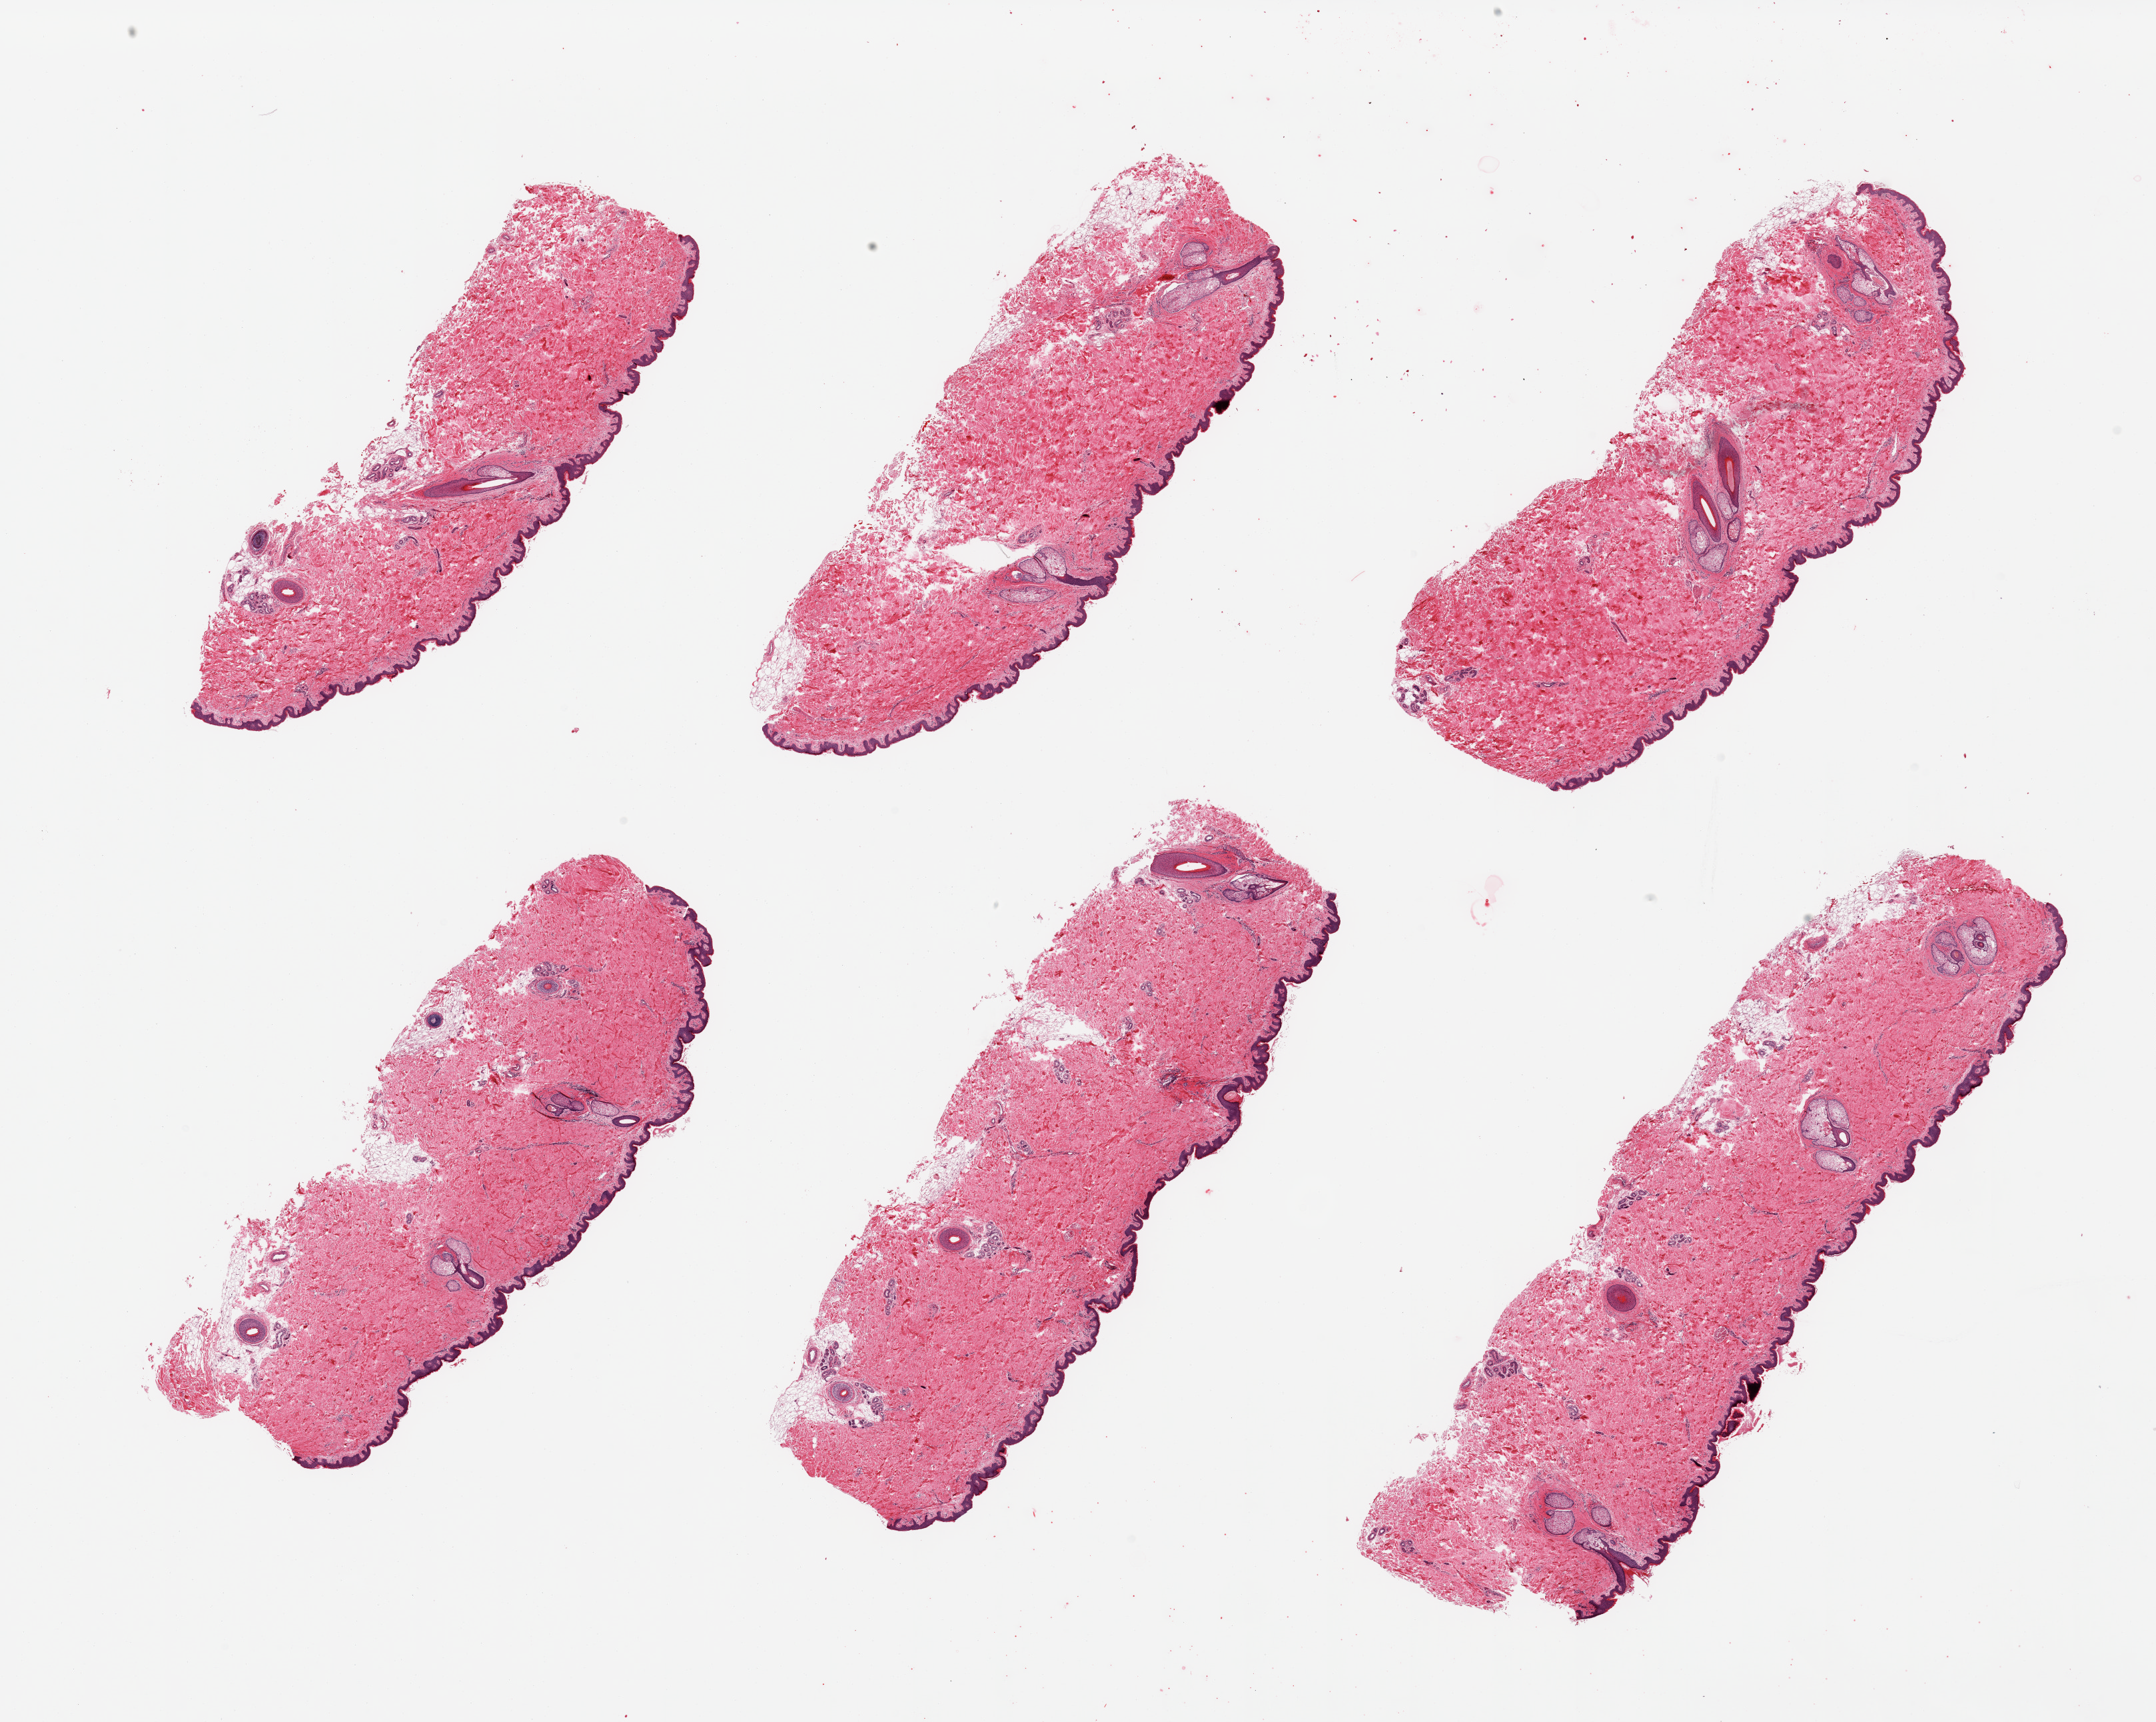
Digitized hematoxylin and eosin (H&E)-stained section, whole scanned area (about 25.6 x 20.4 mm, acquisition: 20x scan) shown as a low-resolution overview, PAXgene-fixed paraffin-embedded (PFPE) section, section of skin of suprapubic region (target tissue), tissue donor sample. Donor sex: male.
* review note (as recorded): 6 pieces; essentially well trimmed